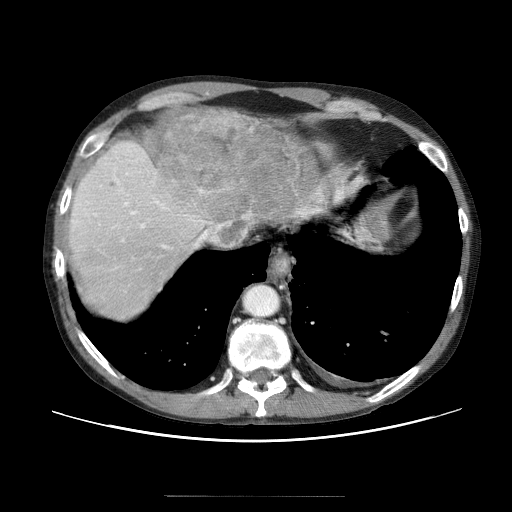
Contrast-enhanced abdominal CT (liver protocol), one axial slice. Position 53 of 69 along the scan axis. 120 kVp. Soft-tissue window (W 400 / L 40 HU). 2.5 mm slice thickness. 512 × 512 image matrix, field of view 380 × 380 mm. Case-level facts recorded for this patient, not image findings: diagnosis: hepatocellular carcinoma (patient treated with transarterial chemoembolisation; whether this scan precedes or follows treatment is not stated here); TNM stage (as recorded): Stage-IVB.
Annotated regions visible in this slice (semi-automatic segmentation, software-assisted and operator-edited):
- liver parenchyma outside the tumour (the mass and vessels are separate outlines, so this box may not span the whole liver): bounding box <66,110,352,330> (left, top, right, bottom; pixels)
- mass: <151,107,355,244>
- liver vessels: <95,173,148,277>